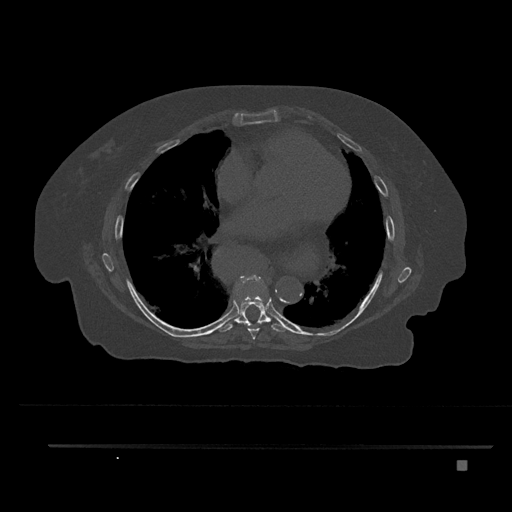
CT including the spine, one axial slice; 120 kVp; bone window (W 1800 / L 400 HU); 0.5 mm slice thickness; 512 × 512 image matrix, field of view 437 × 437 mm. Patient: female, 76 years. Case-level facts recorded for this patient, not image findings: primary cancer: lung; vertebrae with lytic lesions (as recorded): T11, L3.
Outlined on this slice (semi-automatically segmented with operator editing):
- T7 vertebra: box from (x=237, y=275) to (x=264, y=340) px
- T8 vertebra: (x=219, y=294)–(x=288, y=332)